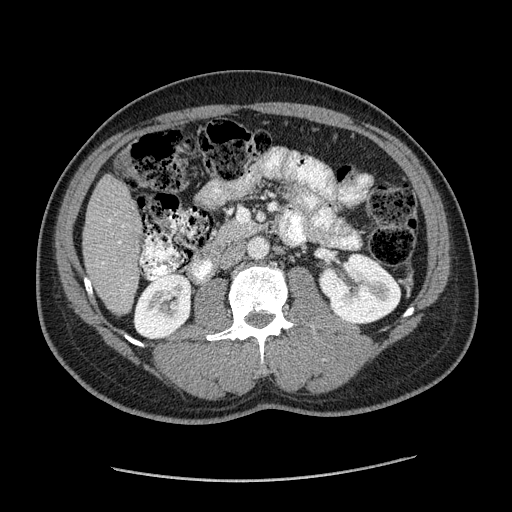
Contrast-enhanced abdominal CT (liver protocol), one axial slice; position 53 of 182 along the scan axis; reconstruction kernel STANDARD; soft-tissue window (W 400 / L 40 HU); 2.5 mm slice thickness; 512 × 512 image matrix. Case-level facts recorded for this patient, not image findings: diagnosis: hepatocellular carcinoma (patient treated with transarterial chemoembolisation; whether this scan precedes or follows treatment is not stated here); TNM stage (as recorded): Stage-I; Child-Pugh class: A; tumour differentiation: well differentiated; tumour nodularity: uninodular.
Outlined on this slice (semi-automatically segmented with operator editing):
- liver parenchyma outside the tumour (the mass and vessels are separate outlines, so this box may not span the whole liver): bounding box [x1, y1, x2, y2] px = [82, 174, 142, 314]
- liver vessels: [109, 220, 124, 244]